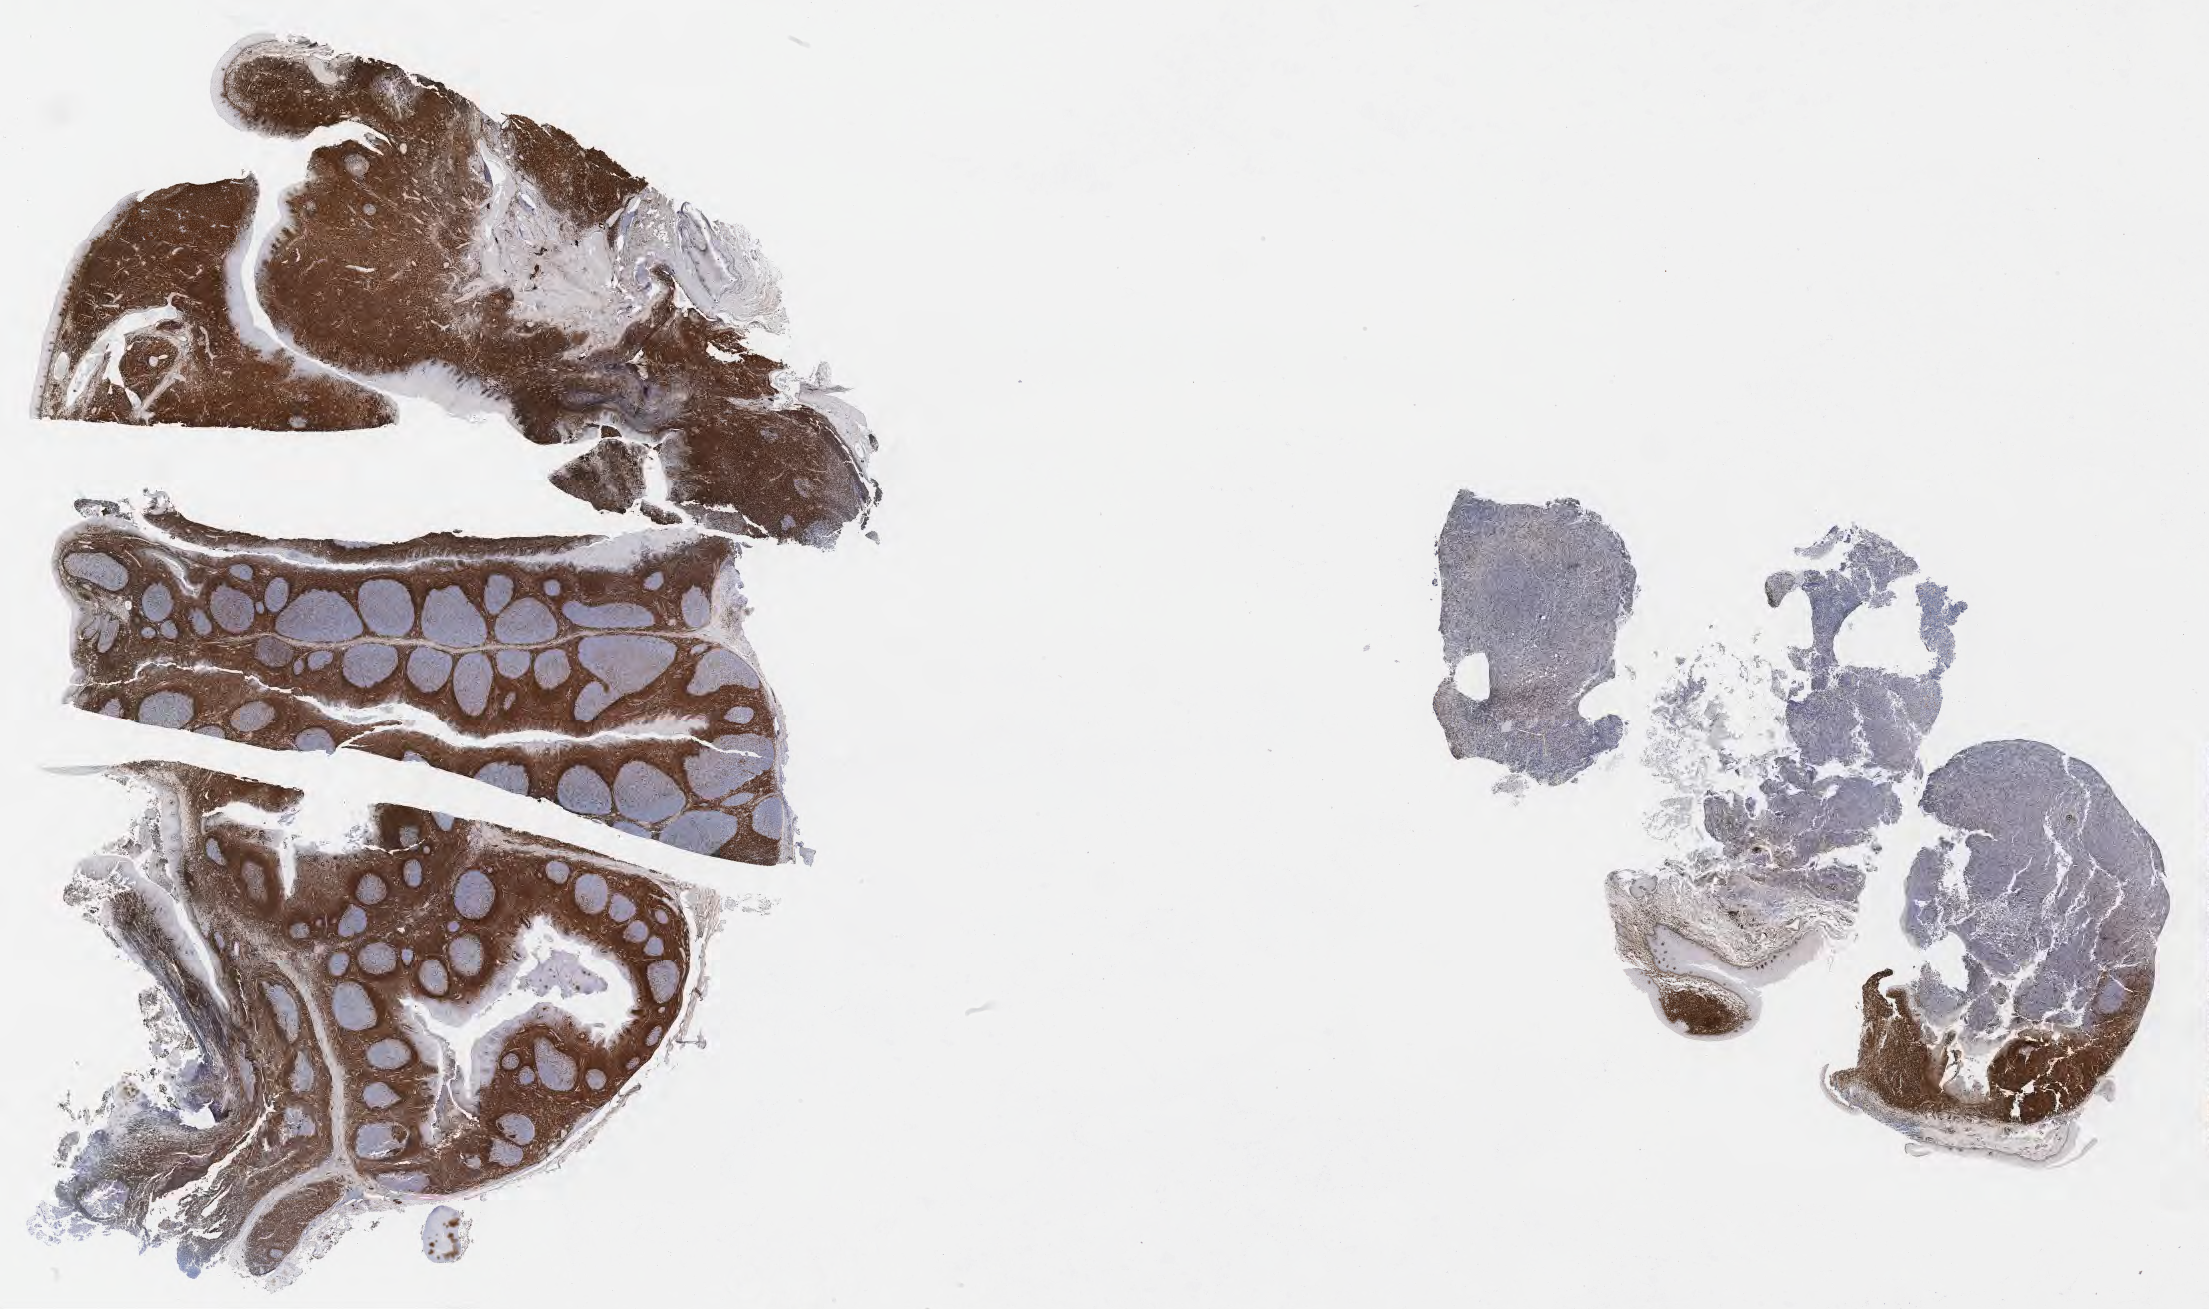
Whole-slide image, immunohistochemical stain for BCL2 — low-resolution overview of the scanned area, about 35.7 x 21.2 mm, specimen: tumor tissue. Patient: male, age 63 years.
Diagnosis: Burkitt lymphoma, NOS.